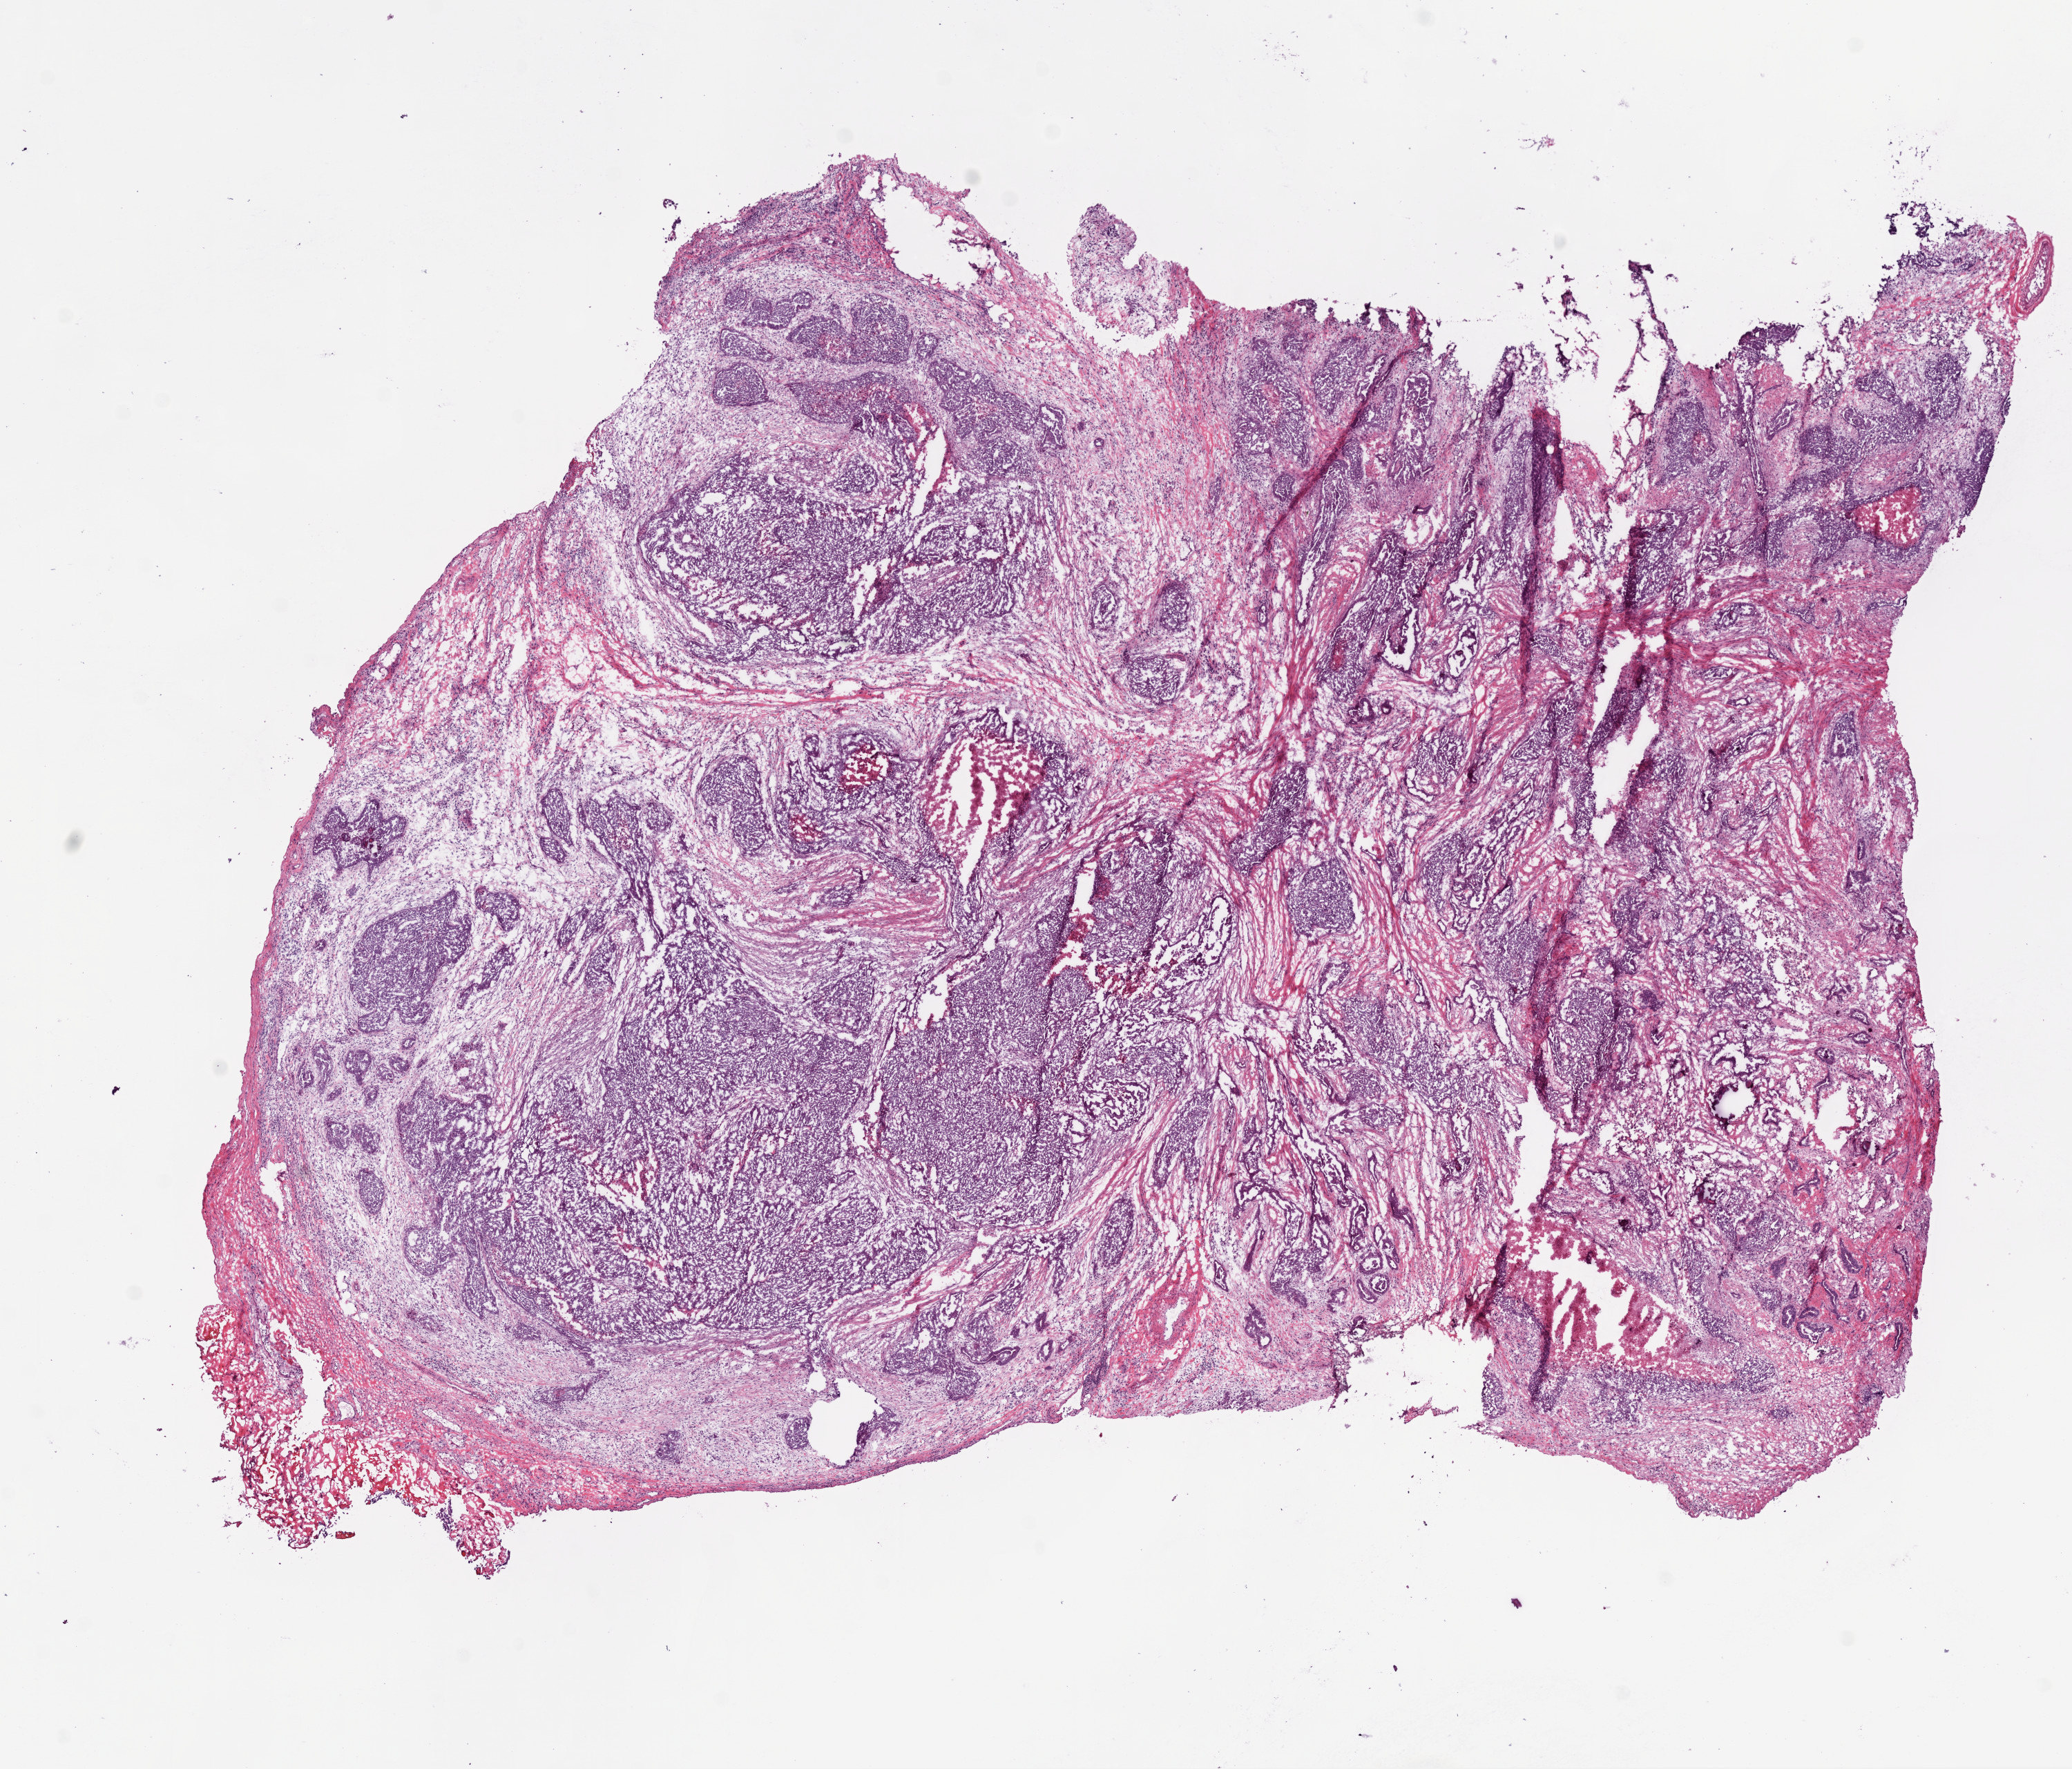
H&E-stained whole-slide image — low-resolution overview of the scanned area, about 12.0 x 10.3 mm (acquisition: 20x scan). Frozen section. Ovary, primary tumour sample. Patient: female, age at initial diagnosis 73 years. Histologic grade: G3 (poorly differentiated). Slide review estimates, as recorded: tumour cells 50%, tumour nuclei 70%, normal cells 0%, stromal cells 45%, necrosis 5%.
* FIGO stage: IIIC
* laterality: bilateral
* histologic diagnosis: Serous cystadenocarcinoma, NOS